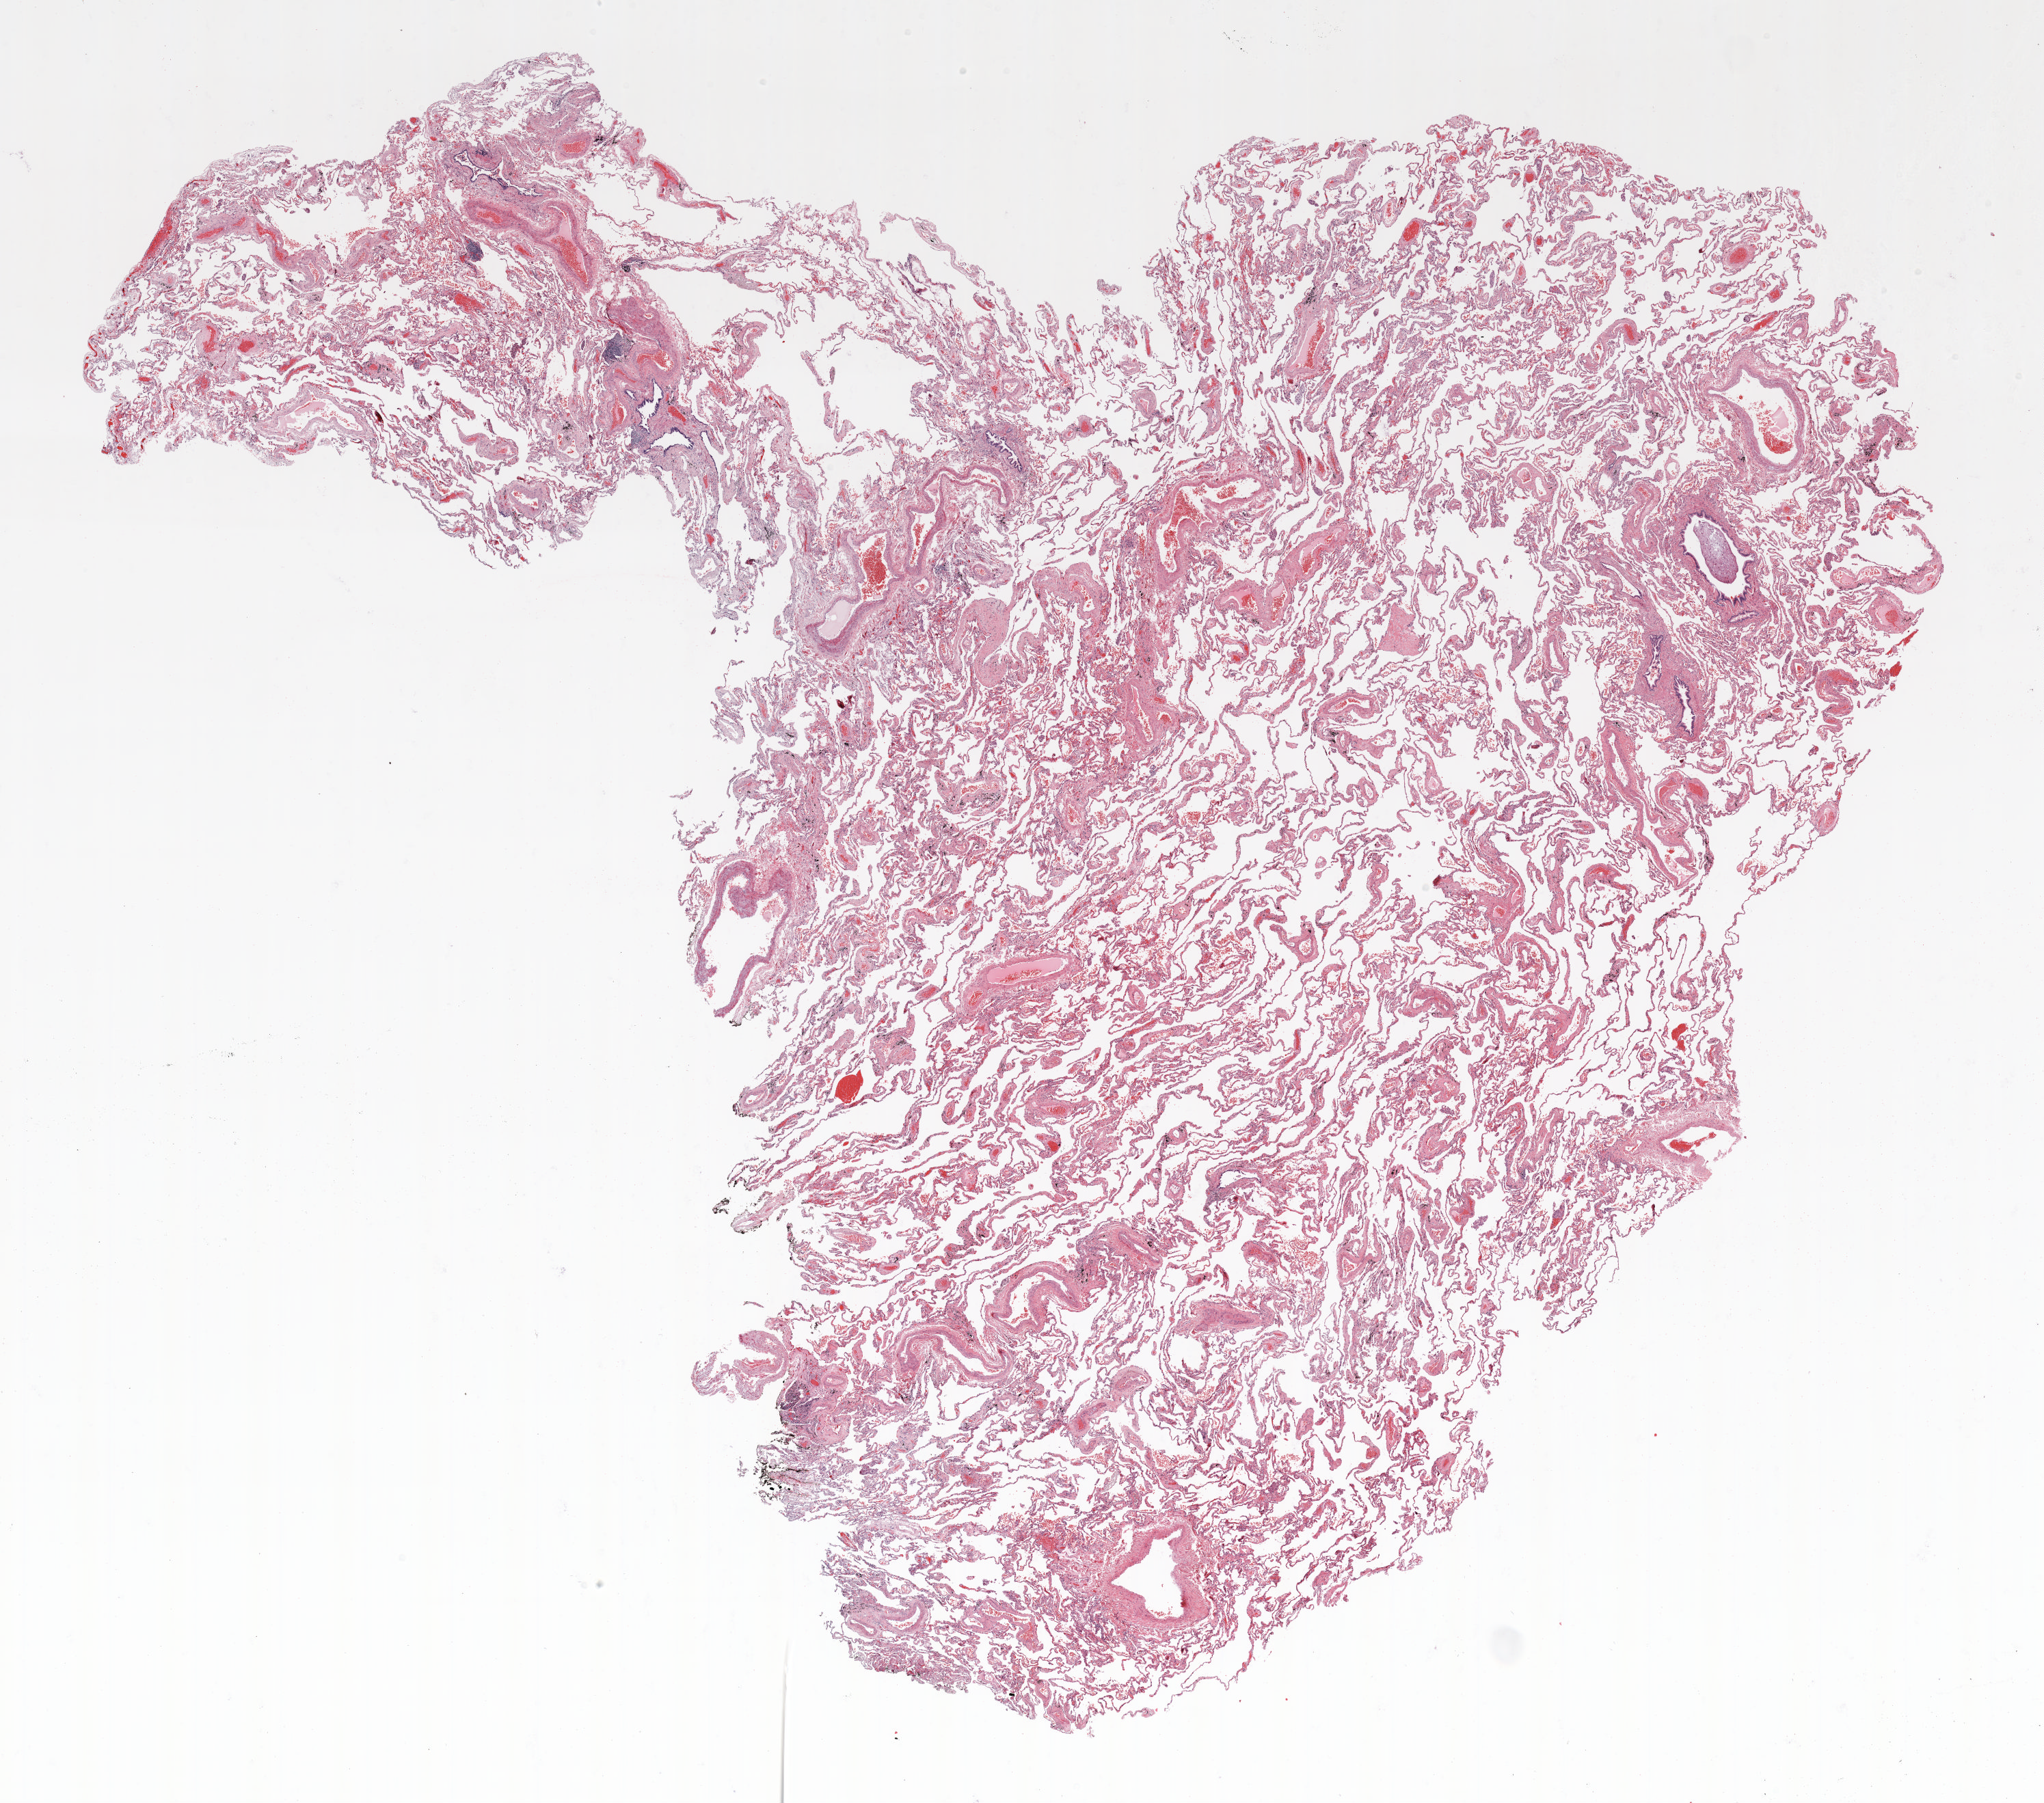
Hematoxylin and eosin (H&E) stained whole-slide image — whole scanned area (about 24.0 x 21.2 mm) shown as a low-resolution overview, FFPE section, lung. Female, age 62 at enrolment. Grade: well differentiated (G1).
* primary tumour location (clinical record): right upper lobe
* participant's lung-cancer diagnosis: Adenocarcinoma, NOS
* stage (AJCC 6th edition): IA
* tumour size (pathology): 7 mm